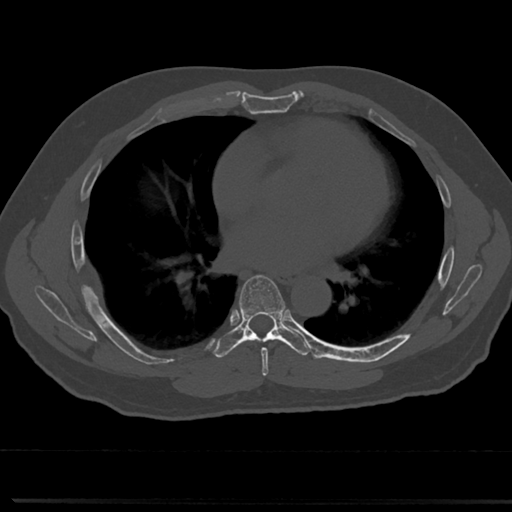
CT including the spine, one axial slice; slice 417 of 817 in the series (ordered by position); 120 kVp; bone window (W 1800 / L 400 HU); 0.5 mm slice thickness; 512 × 512 image matrix, field of view 355 × 355 mm. Male patient, age 61 years. From the clinical record (not read from this slice): primary cancer: prostate.
Outlined on this slice (semi-automatic segmentation, software-assisted and operator-edited):
- T6 vertebra: bounding box <241,281,286,362> (left, top, right, bottom; pixels)
- T7 vertebra: <239,275,286,335>